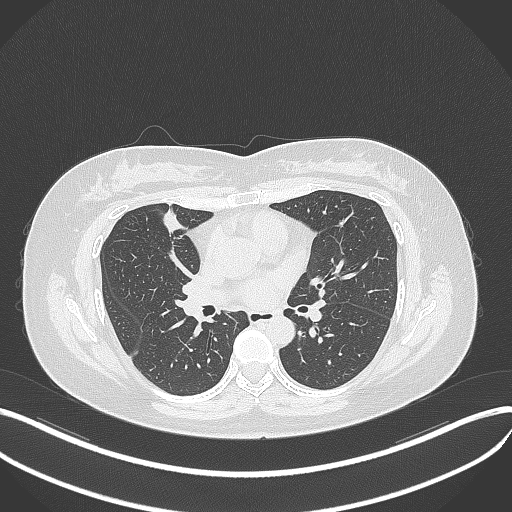
Chest CT, one axial slice; position 166 of 273 along the scan axis; reconstruction kernel B70f; lung window (W 1500 / L -600 HU); 1 mm slice thickness; 512 × 512 image matrix, field of view 400 × 400 mm. Female patient, age 42 years. From the clinical record (not read from this slice): clinical TNM (as recorded): T1b N0 M0.
Structures marked on this image (bounding box drawn by a radiologist):
- lung tumour (recorded histology: adenocarcinoma): box from (x=158, y=205) to (x=187, y=236) px